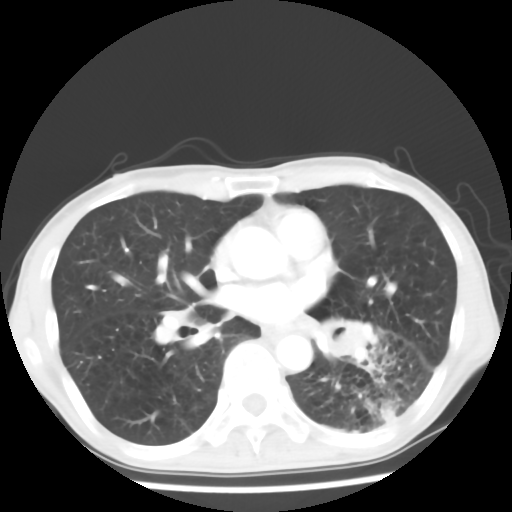
Chest CT, one axial slice. Position 31 of 64 along the scan axis. Reconstruction kernel STANDARD. Lung window (W 1500 / L -600 HU). 512 × 512 image matrix, field of view 313 × 313 mm. Male patient, age 68 years. From the clinical record (not read from this slice): clinical TNM (as recorded): T4 N0 M0.
Annotated regions visible in this slice (rectangle marked by the reading radiologist):
- lung tumour (recorded histology: squamous cell carcinoma): bounding box <325,318,394,373> (left, top, right, bottom; pixels)